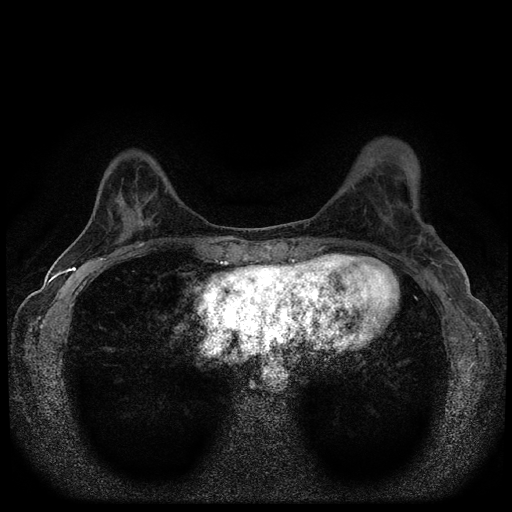
Breast MRI (dynamic contrast-enhanced, multi-phase), one axial slice; slice 34 of 116 in the series (ordered by position); dynamic contrast-enhanced series, time point 2 of 5 at this slice position (early post-contrast); 1.5 T; TE 2.7 ms, TR 5.6 ms; 512 × 512 image matrix, field of view 310 × 310 mm. Female patient, age 40 years.
Annotated regions visible in this slice (semi-automatic segmentation, software-assisted and operator-edited):
- breast lesion (labelled benign in the annotation): bounding box [x1, y1, x2, y2] px = [130, 212, 148, 234]